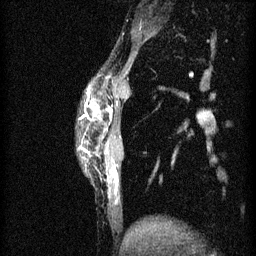
Breast MRI (dynamic contrast-enhanced), one sagittal slice; position 9 of 60 along the scan axis; 3 images stored at this slice position (order not interpretable as contrast timing); 1.5 T; TE 4.2 ms, TR 11 ms; 256 × 256 image matrix, field of view 180 × 180 mm. Patient: female, 40 years.
Structures marked on this image (semi-automatically segmented with operator editing):
- analysis volume of interest (the breast-tissue region the enhancement analysis was run in; not a lesion): box from (x=81, y=82) to (x=131, y=191) px
- tumour enhancement mask (voxels above the 70 % enhancement threshold inside the analysis volume of interest): (x=92, y=108)–(x=116, y=173)